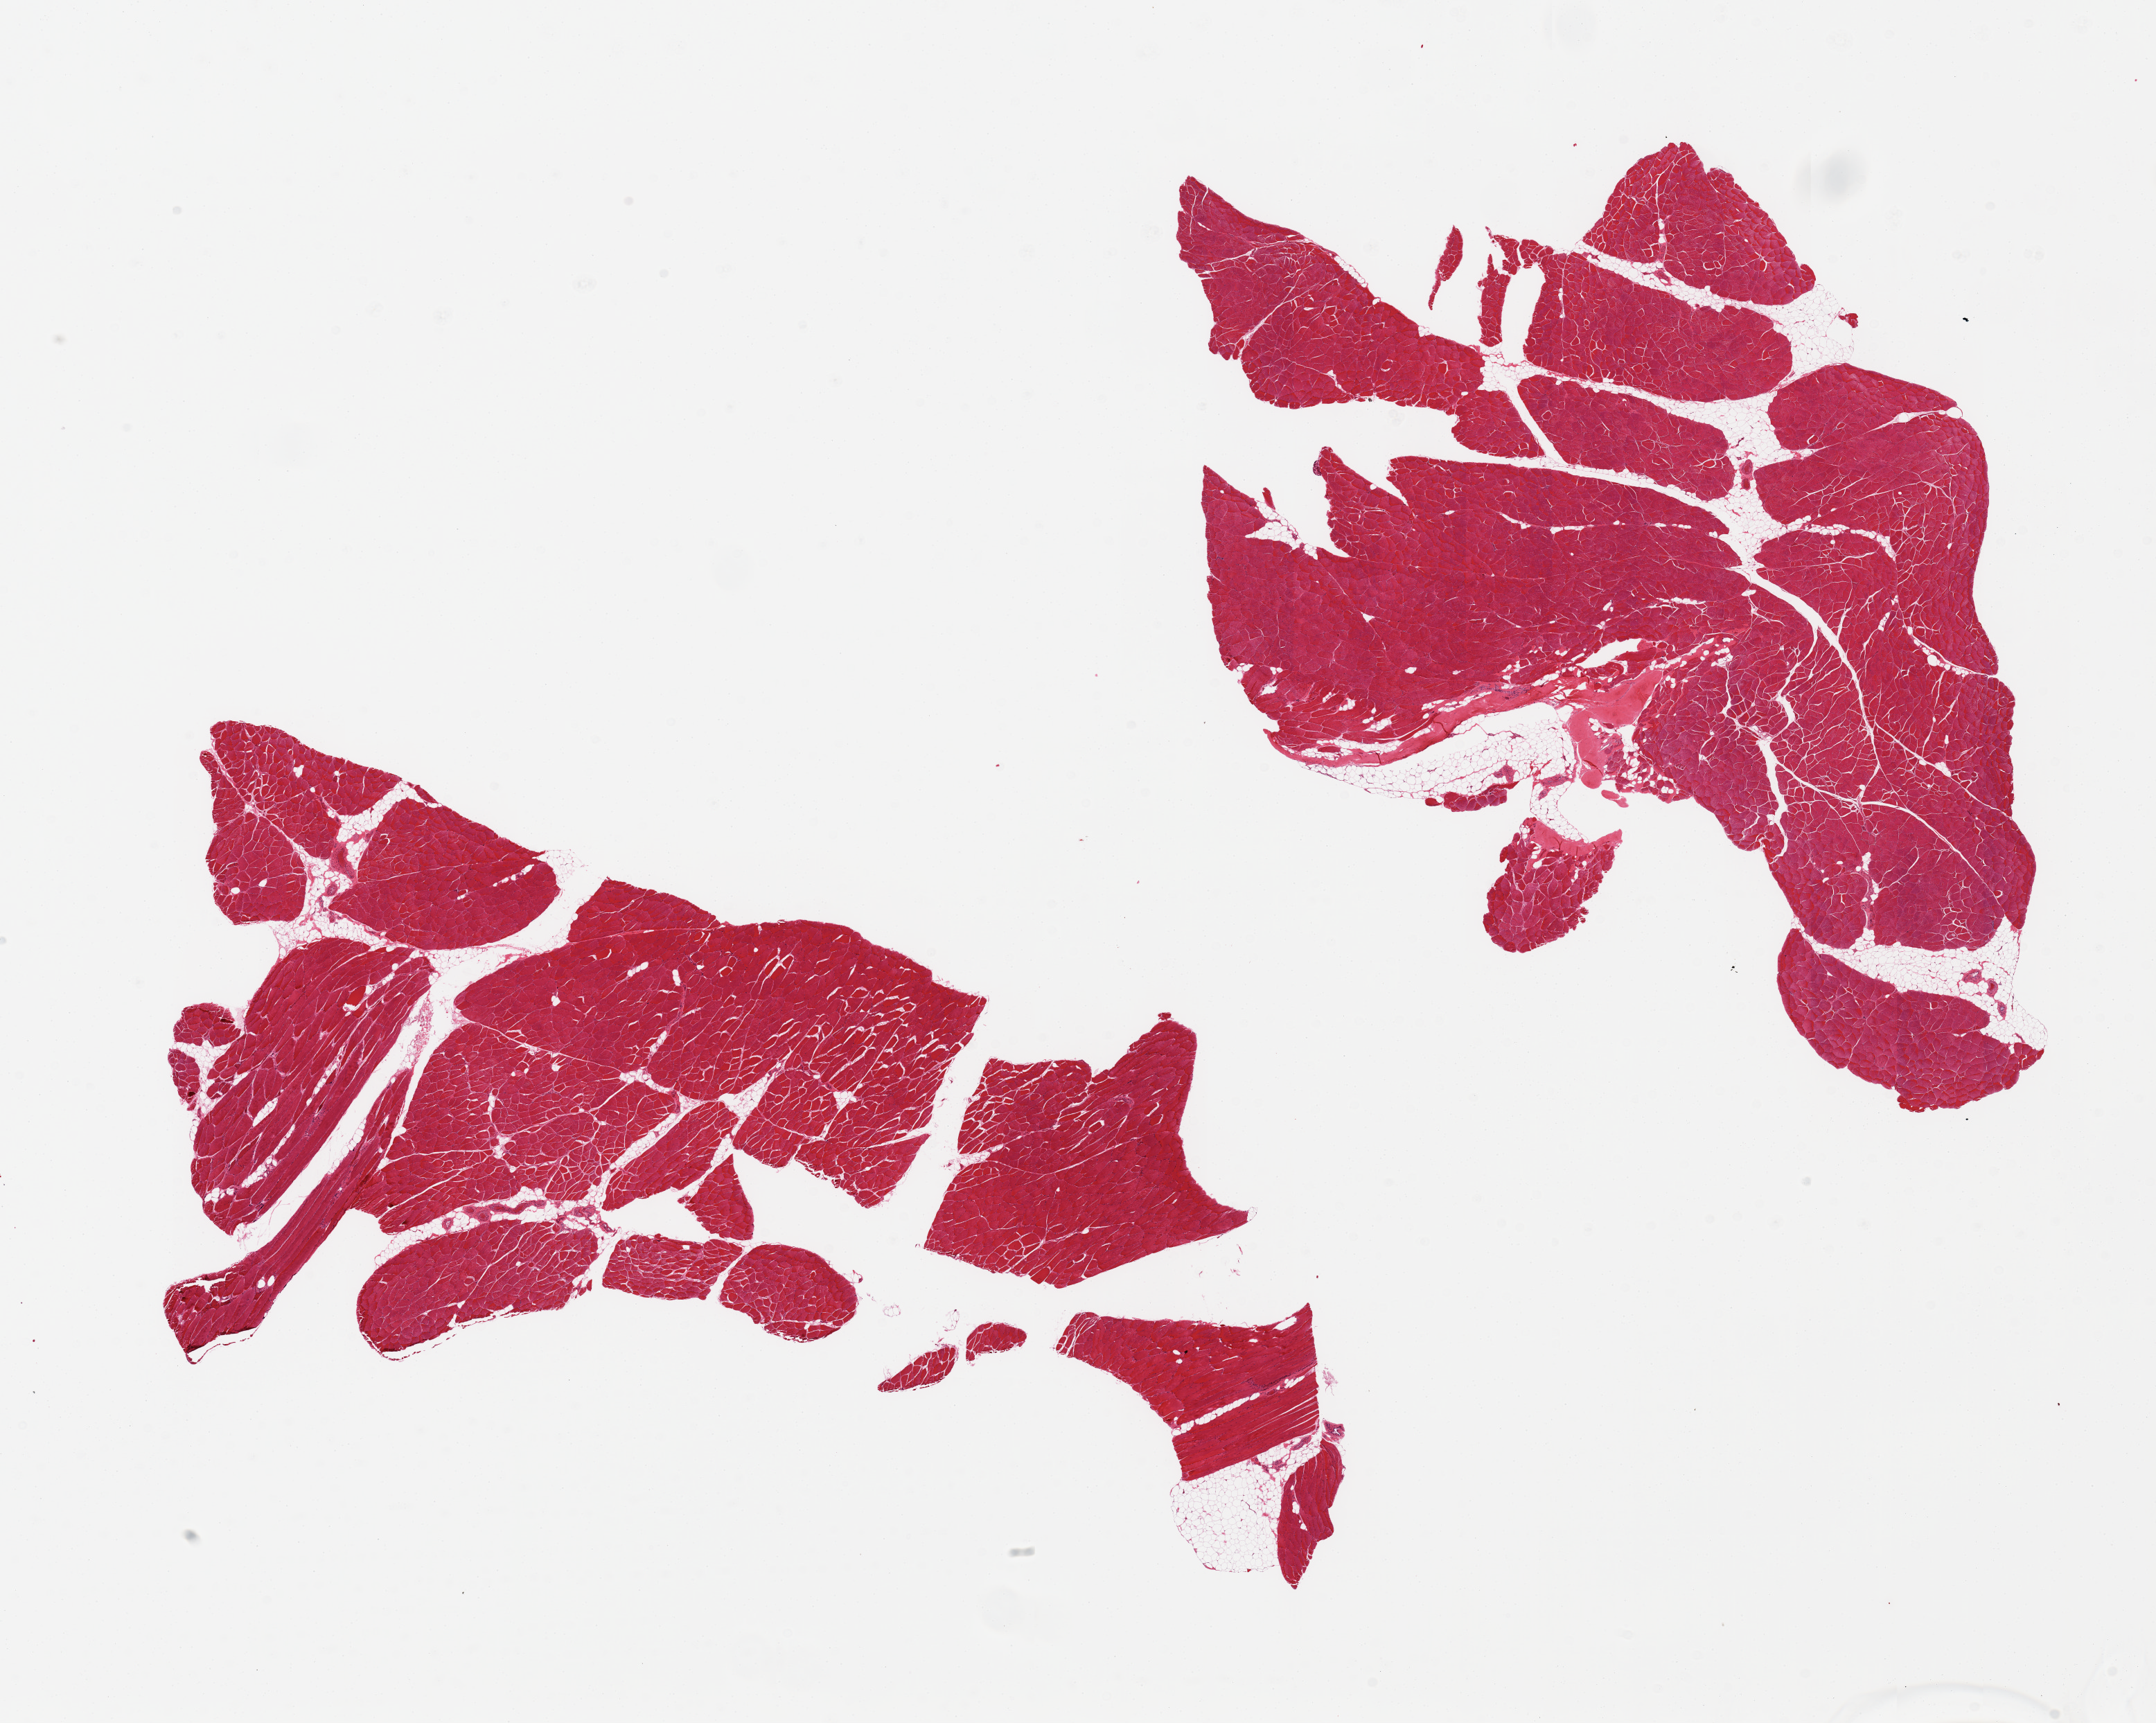
Digitized haematoxylin and eosin-stained section, a low-resolution overview of the entire scanned area, about 24.6 x 19.7 mm, PAXgene-fixed paraffin-embedded (PFPE) section, sampled site (target tissue): skeletal muscle, tissue donor sample. Male donor.
* pathologist's review note for this sample: 2 pieces, ~10% internal fat, one piece includes portion of tendon